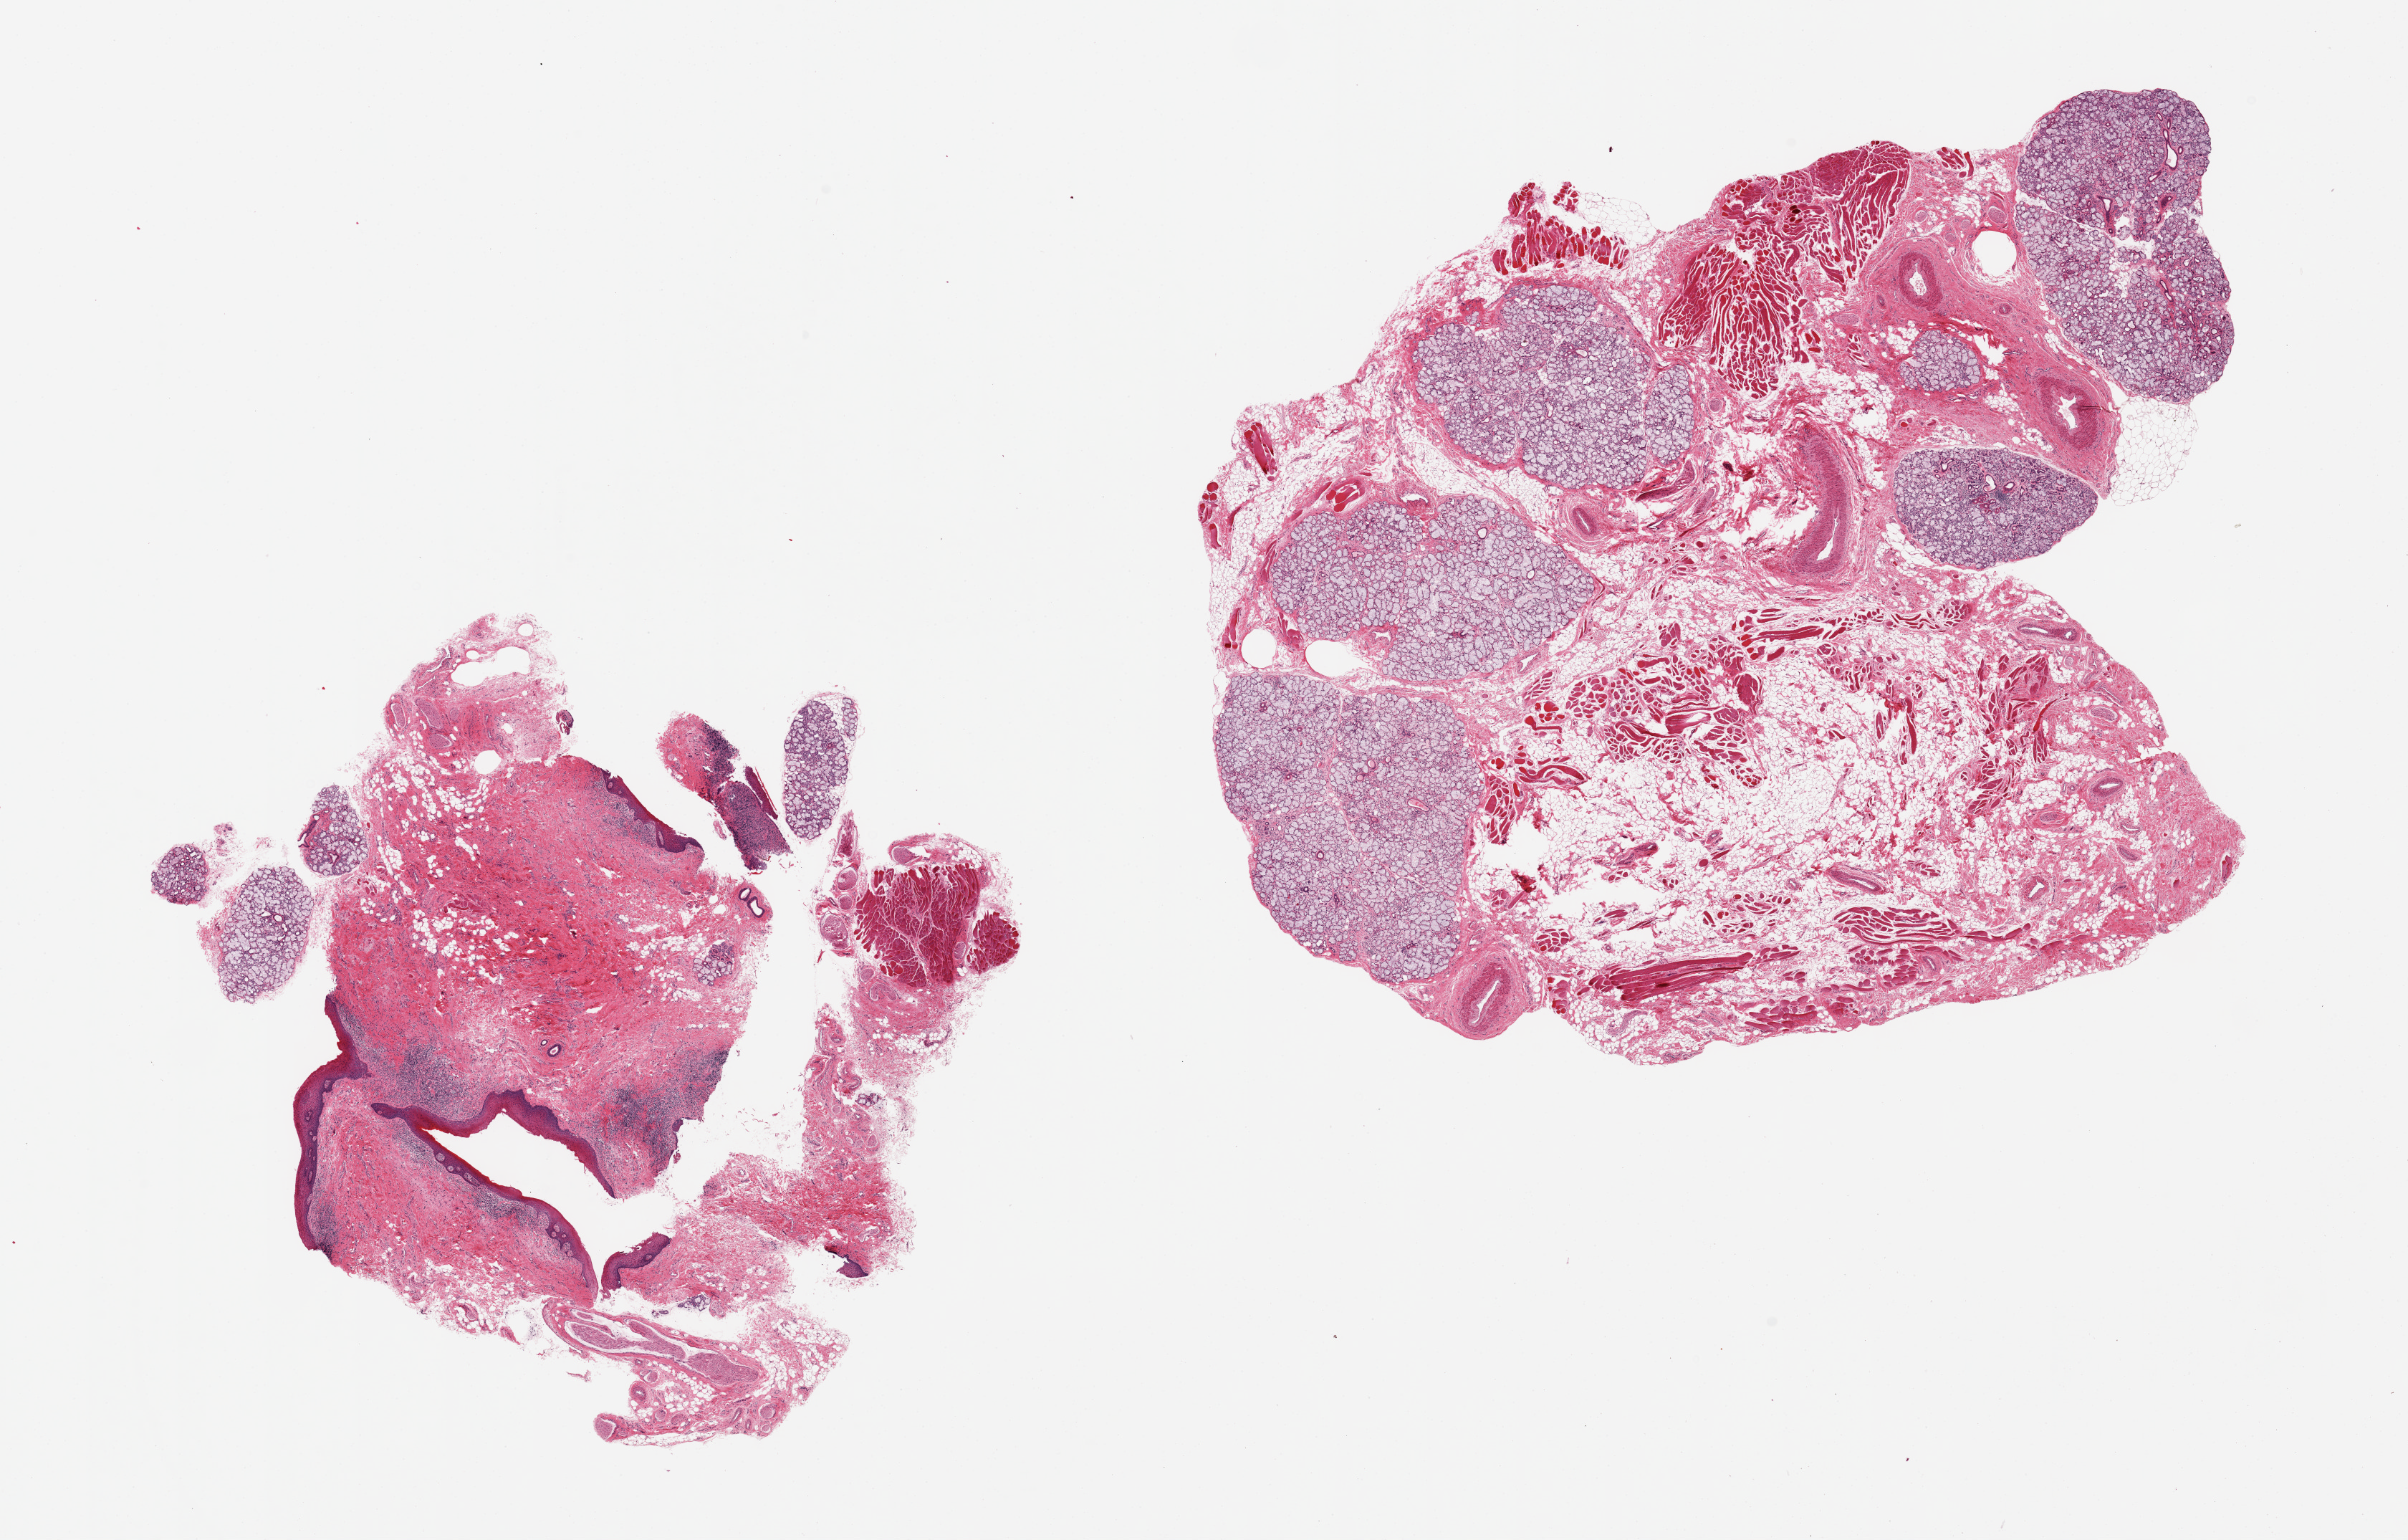
Whole-slide image, haematoxylin and eosin stain, shown as a low-resolution overview of the whole scanned area (about 26.6 x 17.0 mm); PAXgene-fixed, paraffin-embedded tissue; target tissue: minor salivary gland; tissue donor sample. Donor sex: male.
Review note (as recorded): 2 pieces, one predominantly chronically inflamed mucosa, skeletal muscle and nerve tissue with ~10% salivary gland, second is ~40% salivary gland with muscle and fat.